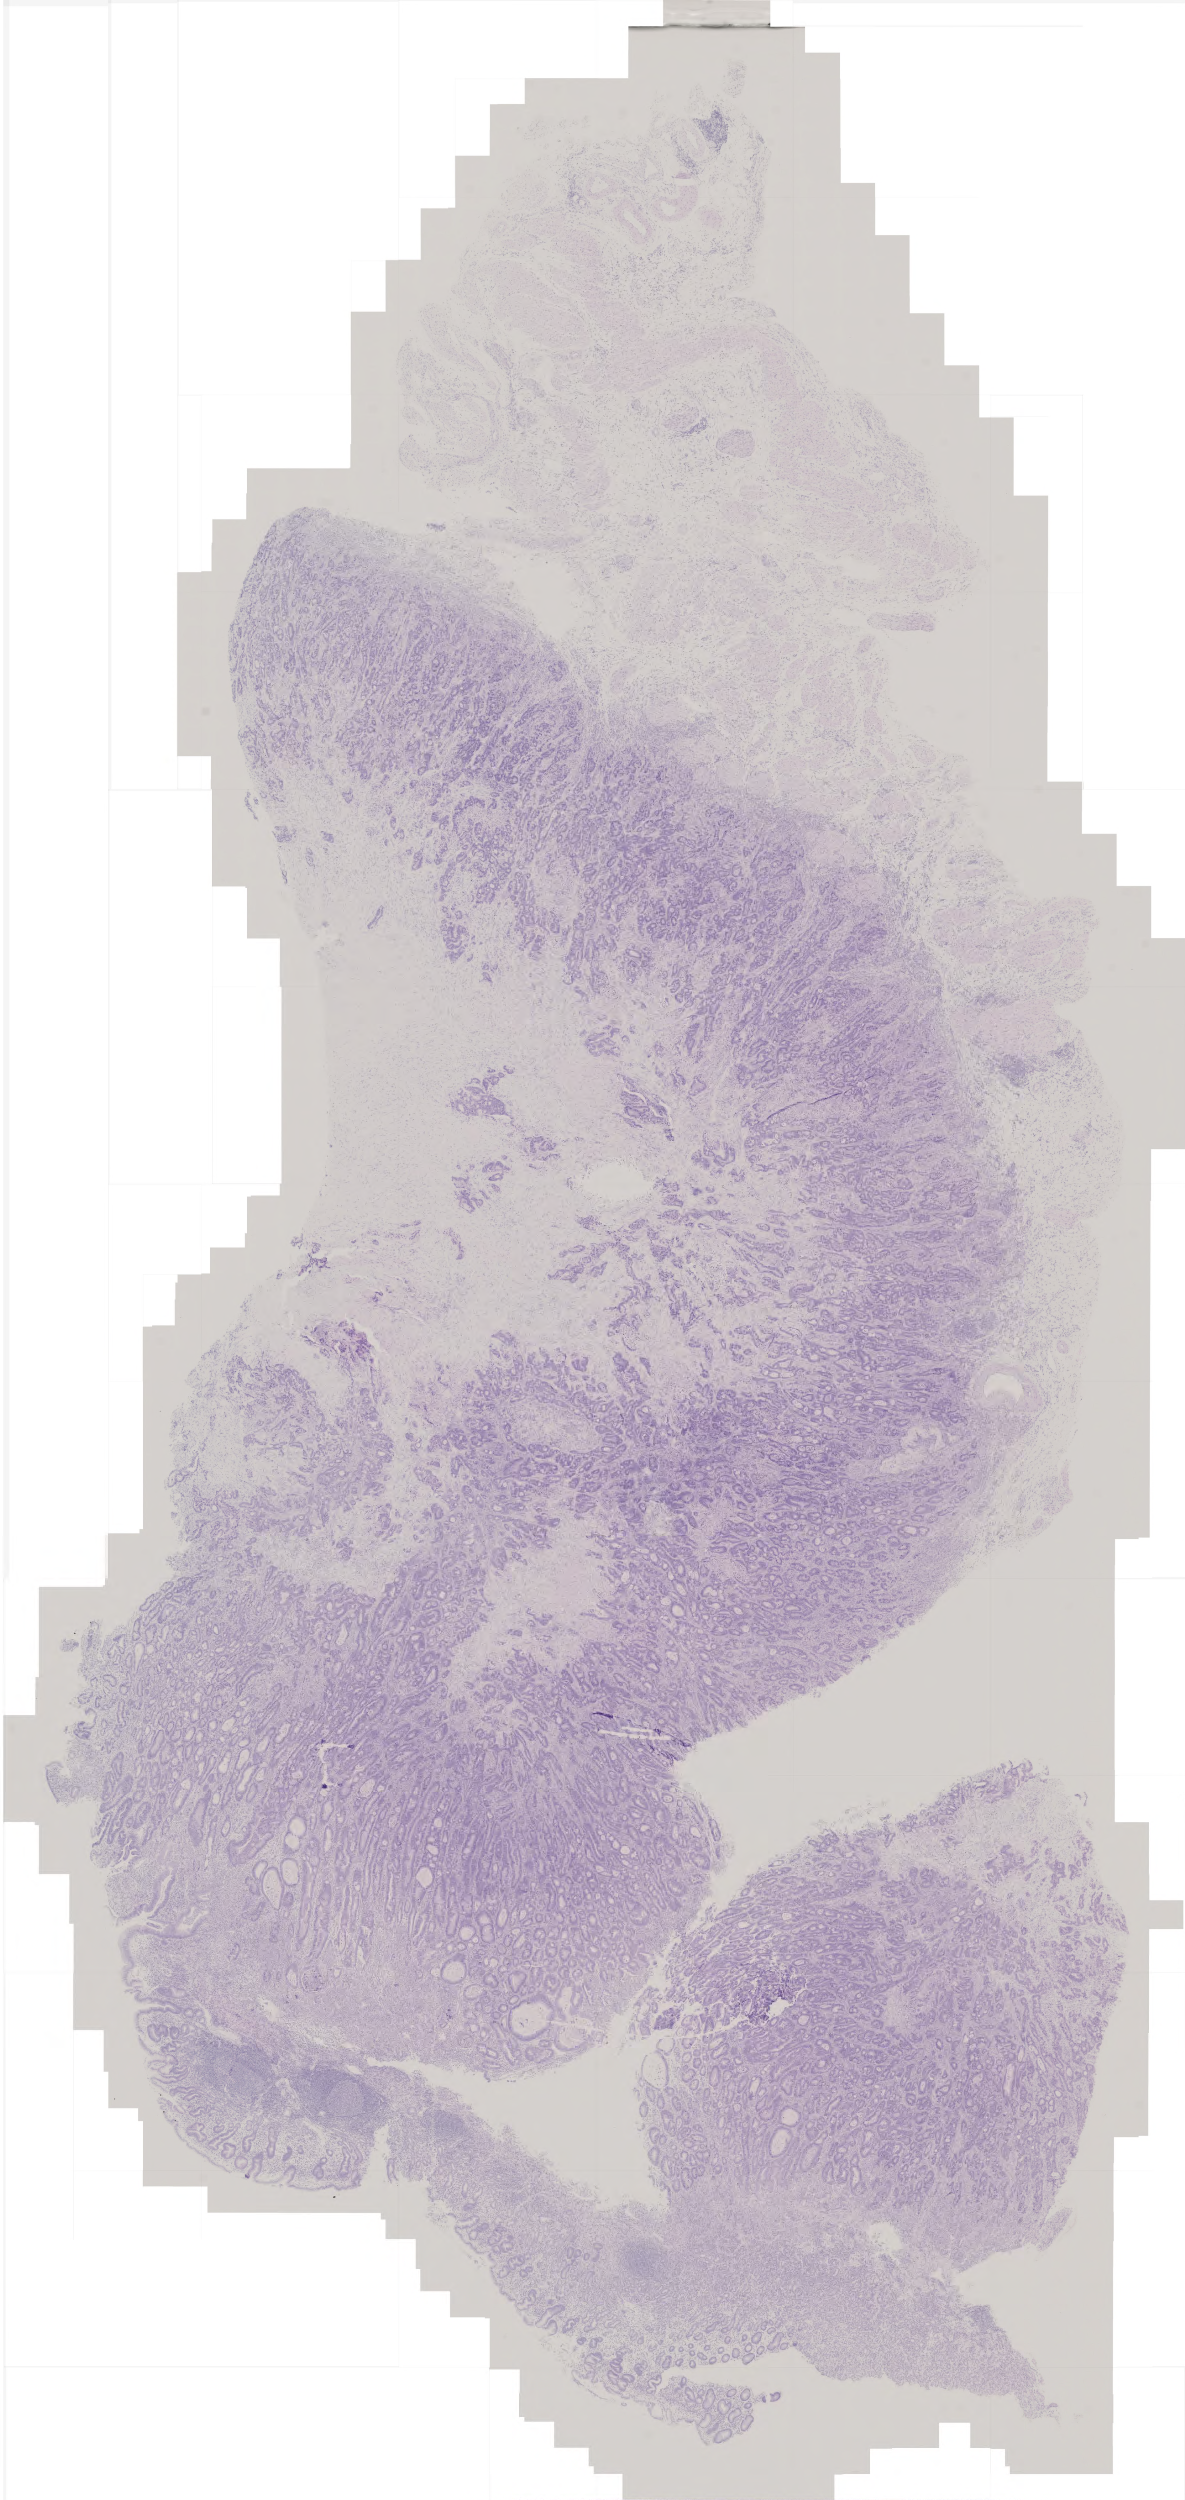
Whole-slide histology image, Hematoxylin and eosin (H&E) stained, low-resolution overview of the scanned area, about 2.4 x 5.0 mm; FFPE section; stomach, primary tumour sample. Patient: male, age at initial diagnosis 83 years. Histologic grade: G2 (moderately differentiated).
• AJCC pathologic stage: II
• histologic diagnosis: Adenocarcinoma, intestinal type (cardia, NOS)